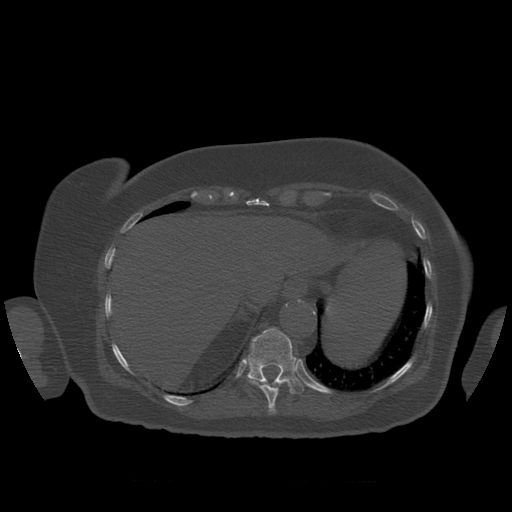
CT including the spine, one axial slice. Position 329 of 399 along the scan axis. Reconstruction kernel STANDARD. 120 kVp. Bone window (W 1800 / L 400 HU). 1.25 mm slice thickness. 512 × 512 image matrix, field of view 404 × 404 mm. Patient age 81 years. From the clinical record (not read from this slice): primary cancer: renal.
Structures marked on this image (semi-automatic segmentation, software-assisted and operator-edited):
- T10 vertebra: box from (x=247, y=376) to (x=292, y=414) px
- T11 vertebra: (x=247, y=328)–(x=304, y=395)